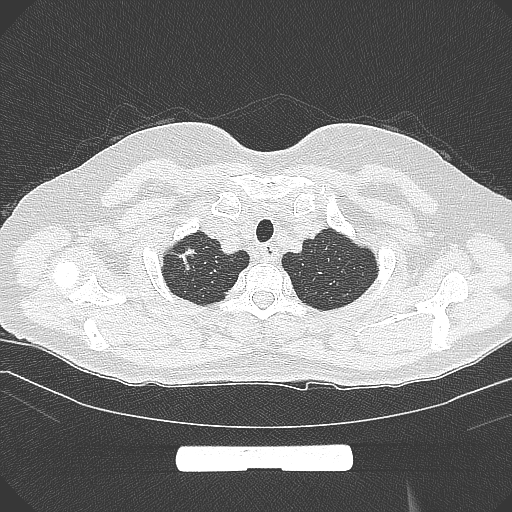
Chest CT, one axial slice. Slice 265 of 295 in the series (ordered by position). Lung window (W 1500 / L -600 HU). 1 mm slice thickness. 512 × 512 image matrix, field of view 369 × 369 mm. Female patient, age 58 years. From the clinical record (not read from this slice): clinical TNM (as recorded): T1b N0 M0; histopathological grade: G2-3.
Outlined on this slice (bounding box drawn by a radiologist):
- lung tumour (recorded histology: adenocarcinoma): bounding box <172,242,204,280> (left, top, right, bottom; pixels)